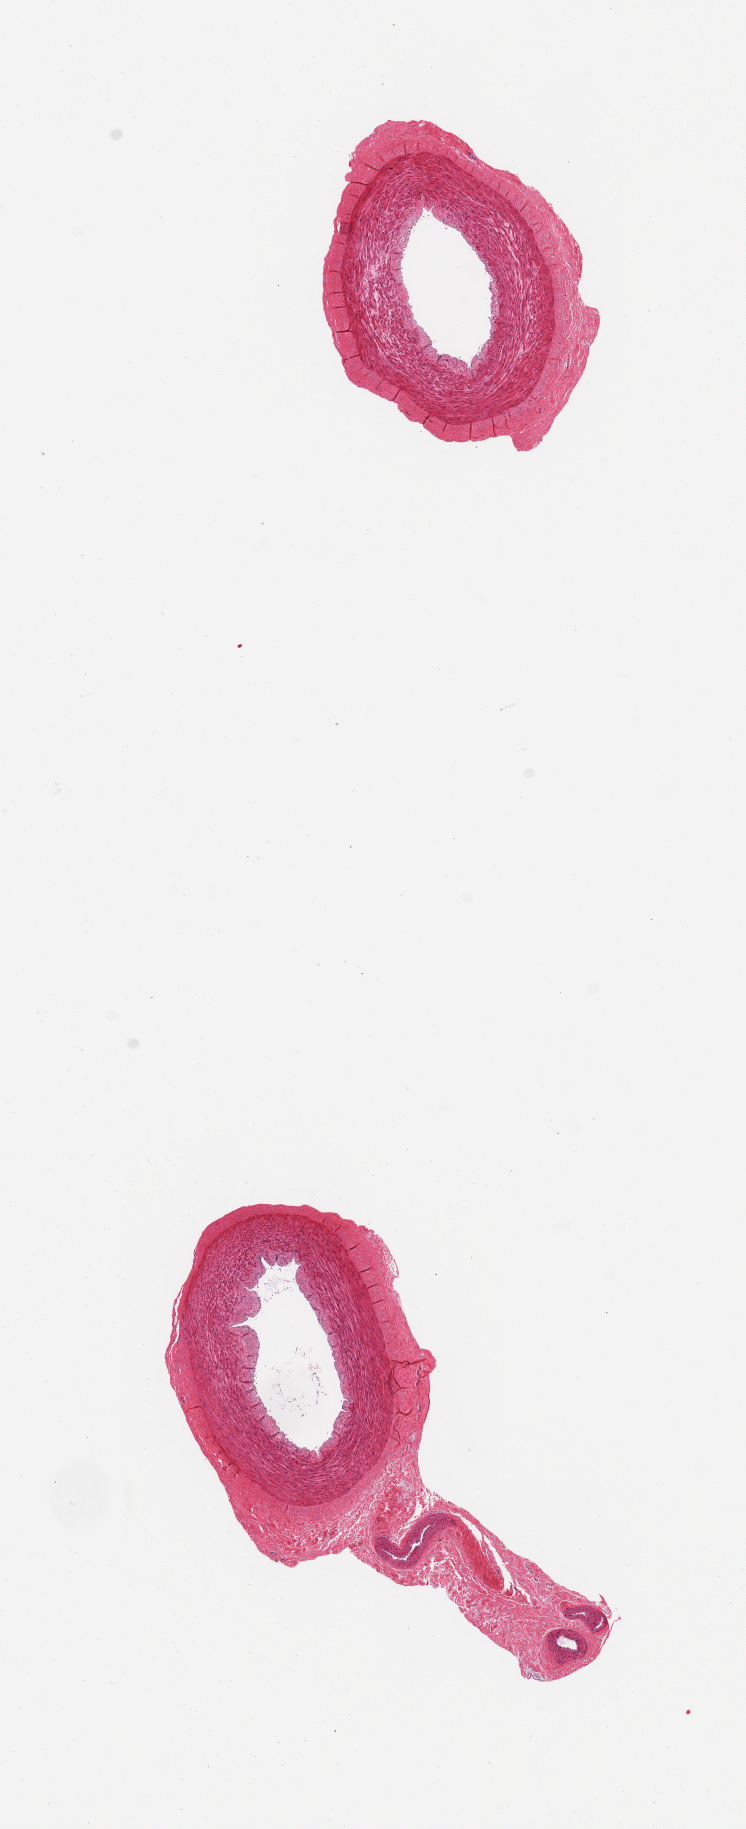
Whole-slide image, haematoxylin and eosin stain, shown as a low-resolution overview of the whole scanned area (about 5.9 x 14.5 mm, from a 20x scan); PAXgene-fixed, paraffin-embedded tissue; target tissue: tibial artery; donor tissue sample. Donor sex: male.
Reviewer comment on this tissue sample: 2 pieces; lumina open; adherent adventitia and smaller vessels.